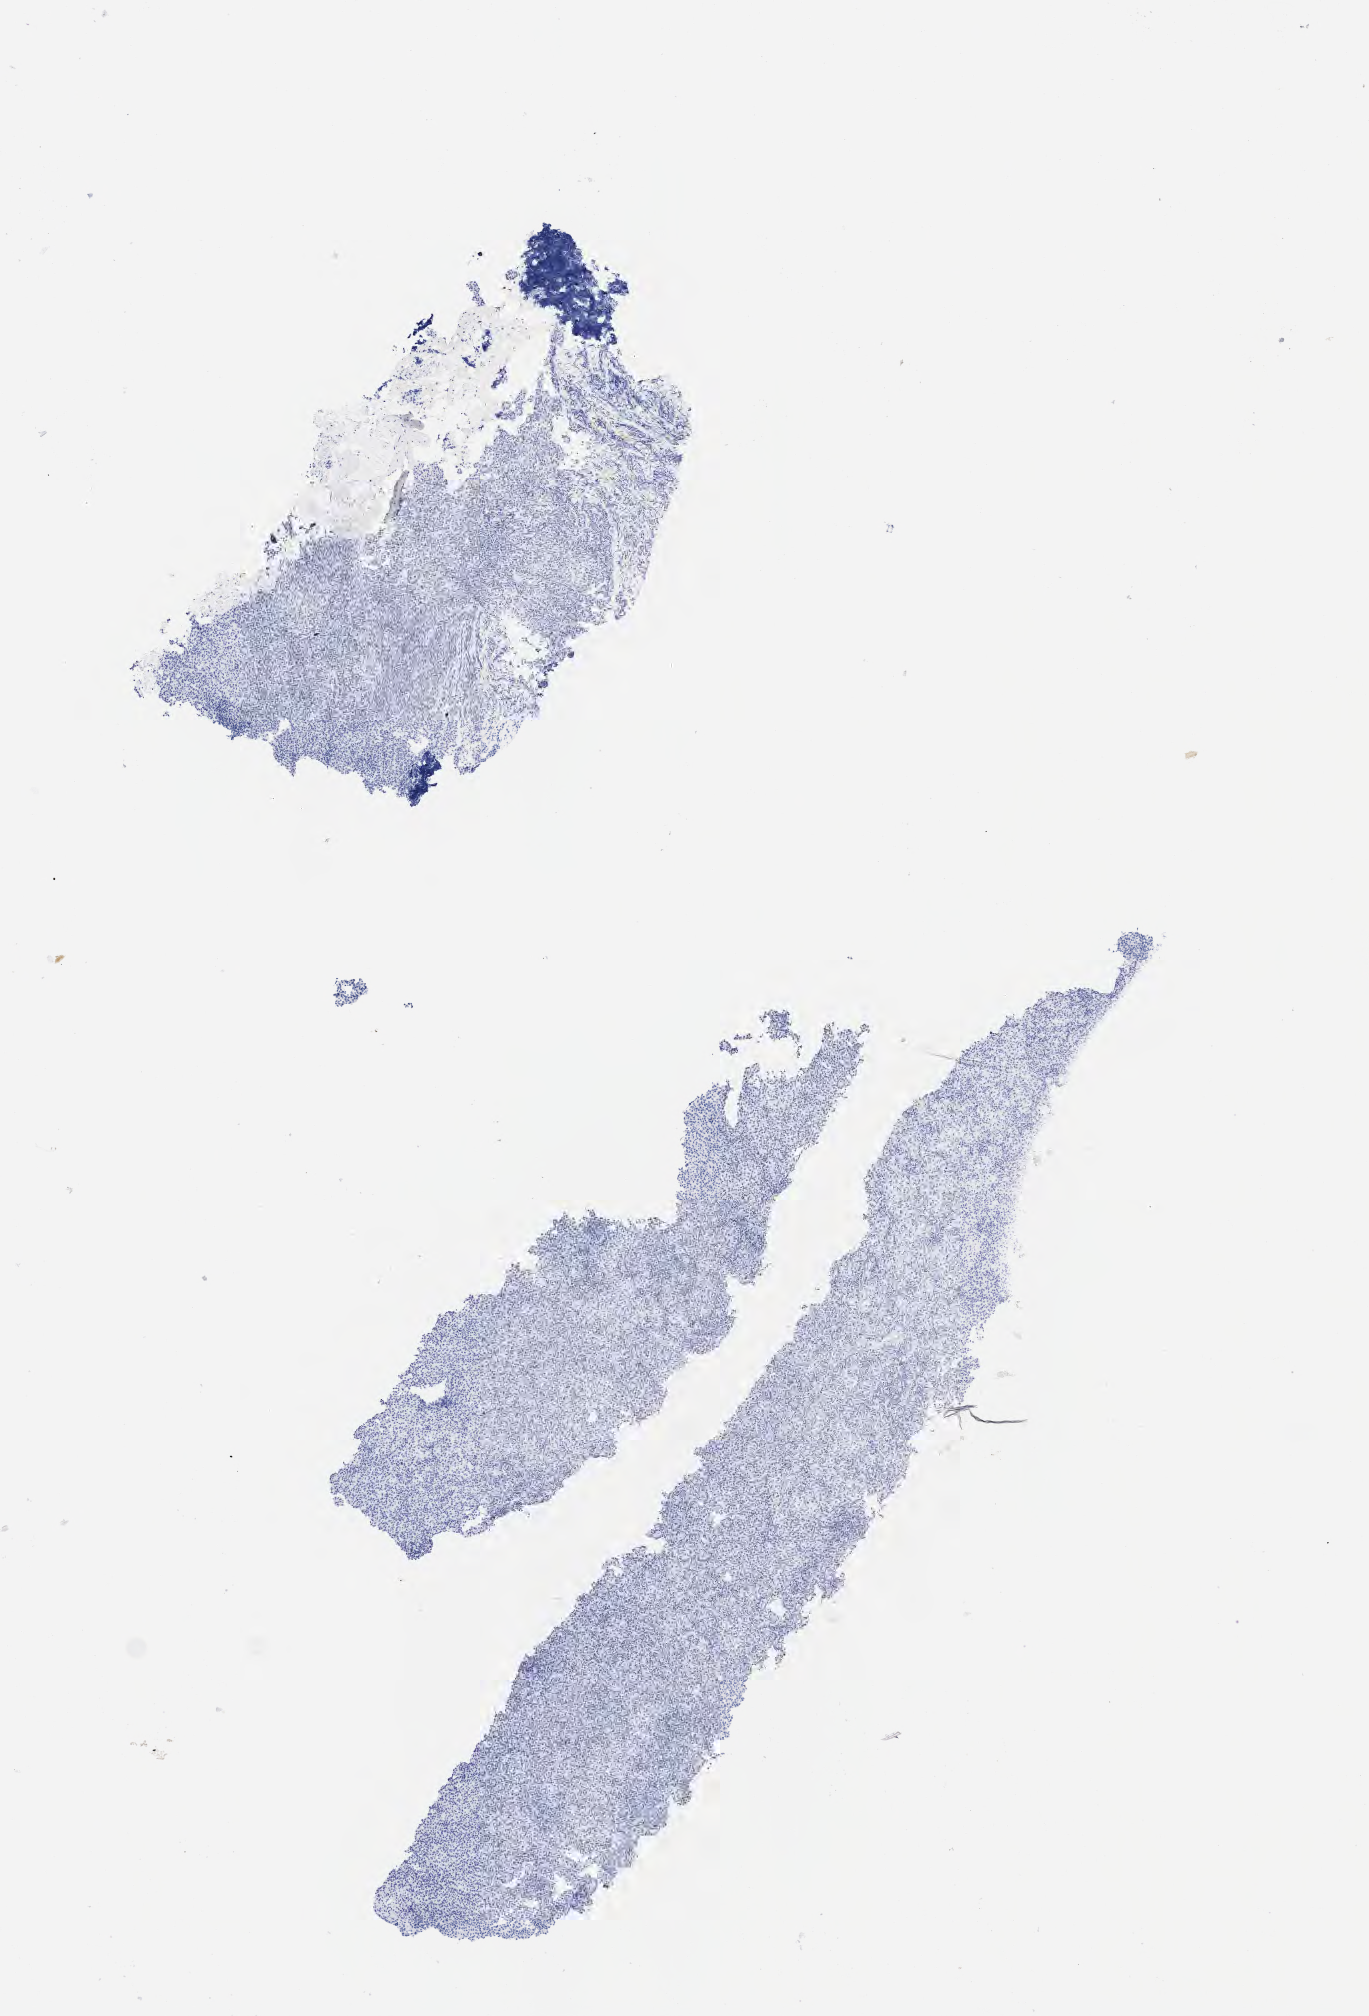
Immunohistochemistry (IHC) whole-slide image stained for synaptophysin, whole scanned area (about 5.5 x 8.1 mm) shown as a low-resolution overview. Tumor tissue. Site: lung (left). Patient: female, age 65 years.
Histologic diagnosis: Non-small cell carcinoma.